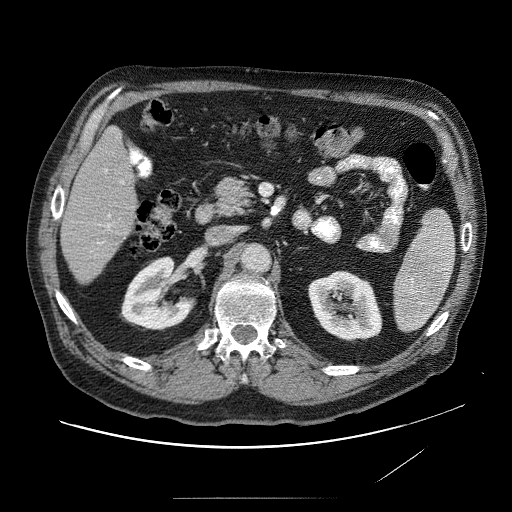
Contrast-enhanced abdominal CT (liver protocol), one axial slice; position 24 of 89 along the scan axis; reconstruction kernel STANDARD; 120 kVp; soft-tissue window (W 400 / L 40 HU); 2.5 mm slice thickness; 512 × 512 image matrix, field of view 420 × 420 mm. Case-level facts recorded for this patient, not image findings: diagnosis: hepatocellular carcinoma (patient treated with transarterial chemoembolisation; whether this scan precedes or follows treatment is not stated here); TNM stage (as recorded): Stage-IVA; Child-Pugh class: A; tumour differentiation: moderately differentiated; tumour nodularity: multinodular.
Annotated regions visible in this slice (semi-automatically segmented with operator editing):
- liver parenchyma outside the tumour (the mass and vessels are separate outlines, so this box may not span the whole liver): bounding box (x1, y1, x2, y2) in pixels: (60, 120, 144, 288)
- liver vessels: (109, 182, 130, 228)